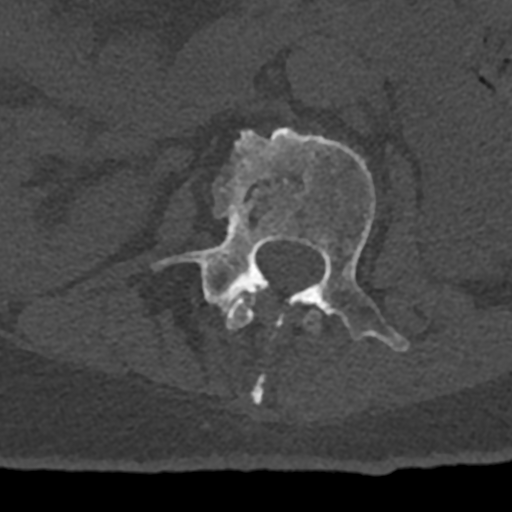
CT including the spine, one axial slice. Position 389 of 797 along the scan axis. Bone window (W 1800 / L 400 HU). 0.5 mm slice thickness. 512 × 512 image matrix. Patient: male, 74 years. Case-level facts recorded for this patient, not image findings: primary cancer: renal; vertebrae with lytic lesions (as recorded): T10, L1, L2, L3, L4, L5.
Structures marked on this image (semi-automatically segmented with operator editing):
- L1 vertebra: bounding box [x1, y1, x2, y2] px = [226, 290, 320, 332]
- L2 vertebra: [152, 127, 409, 404]